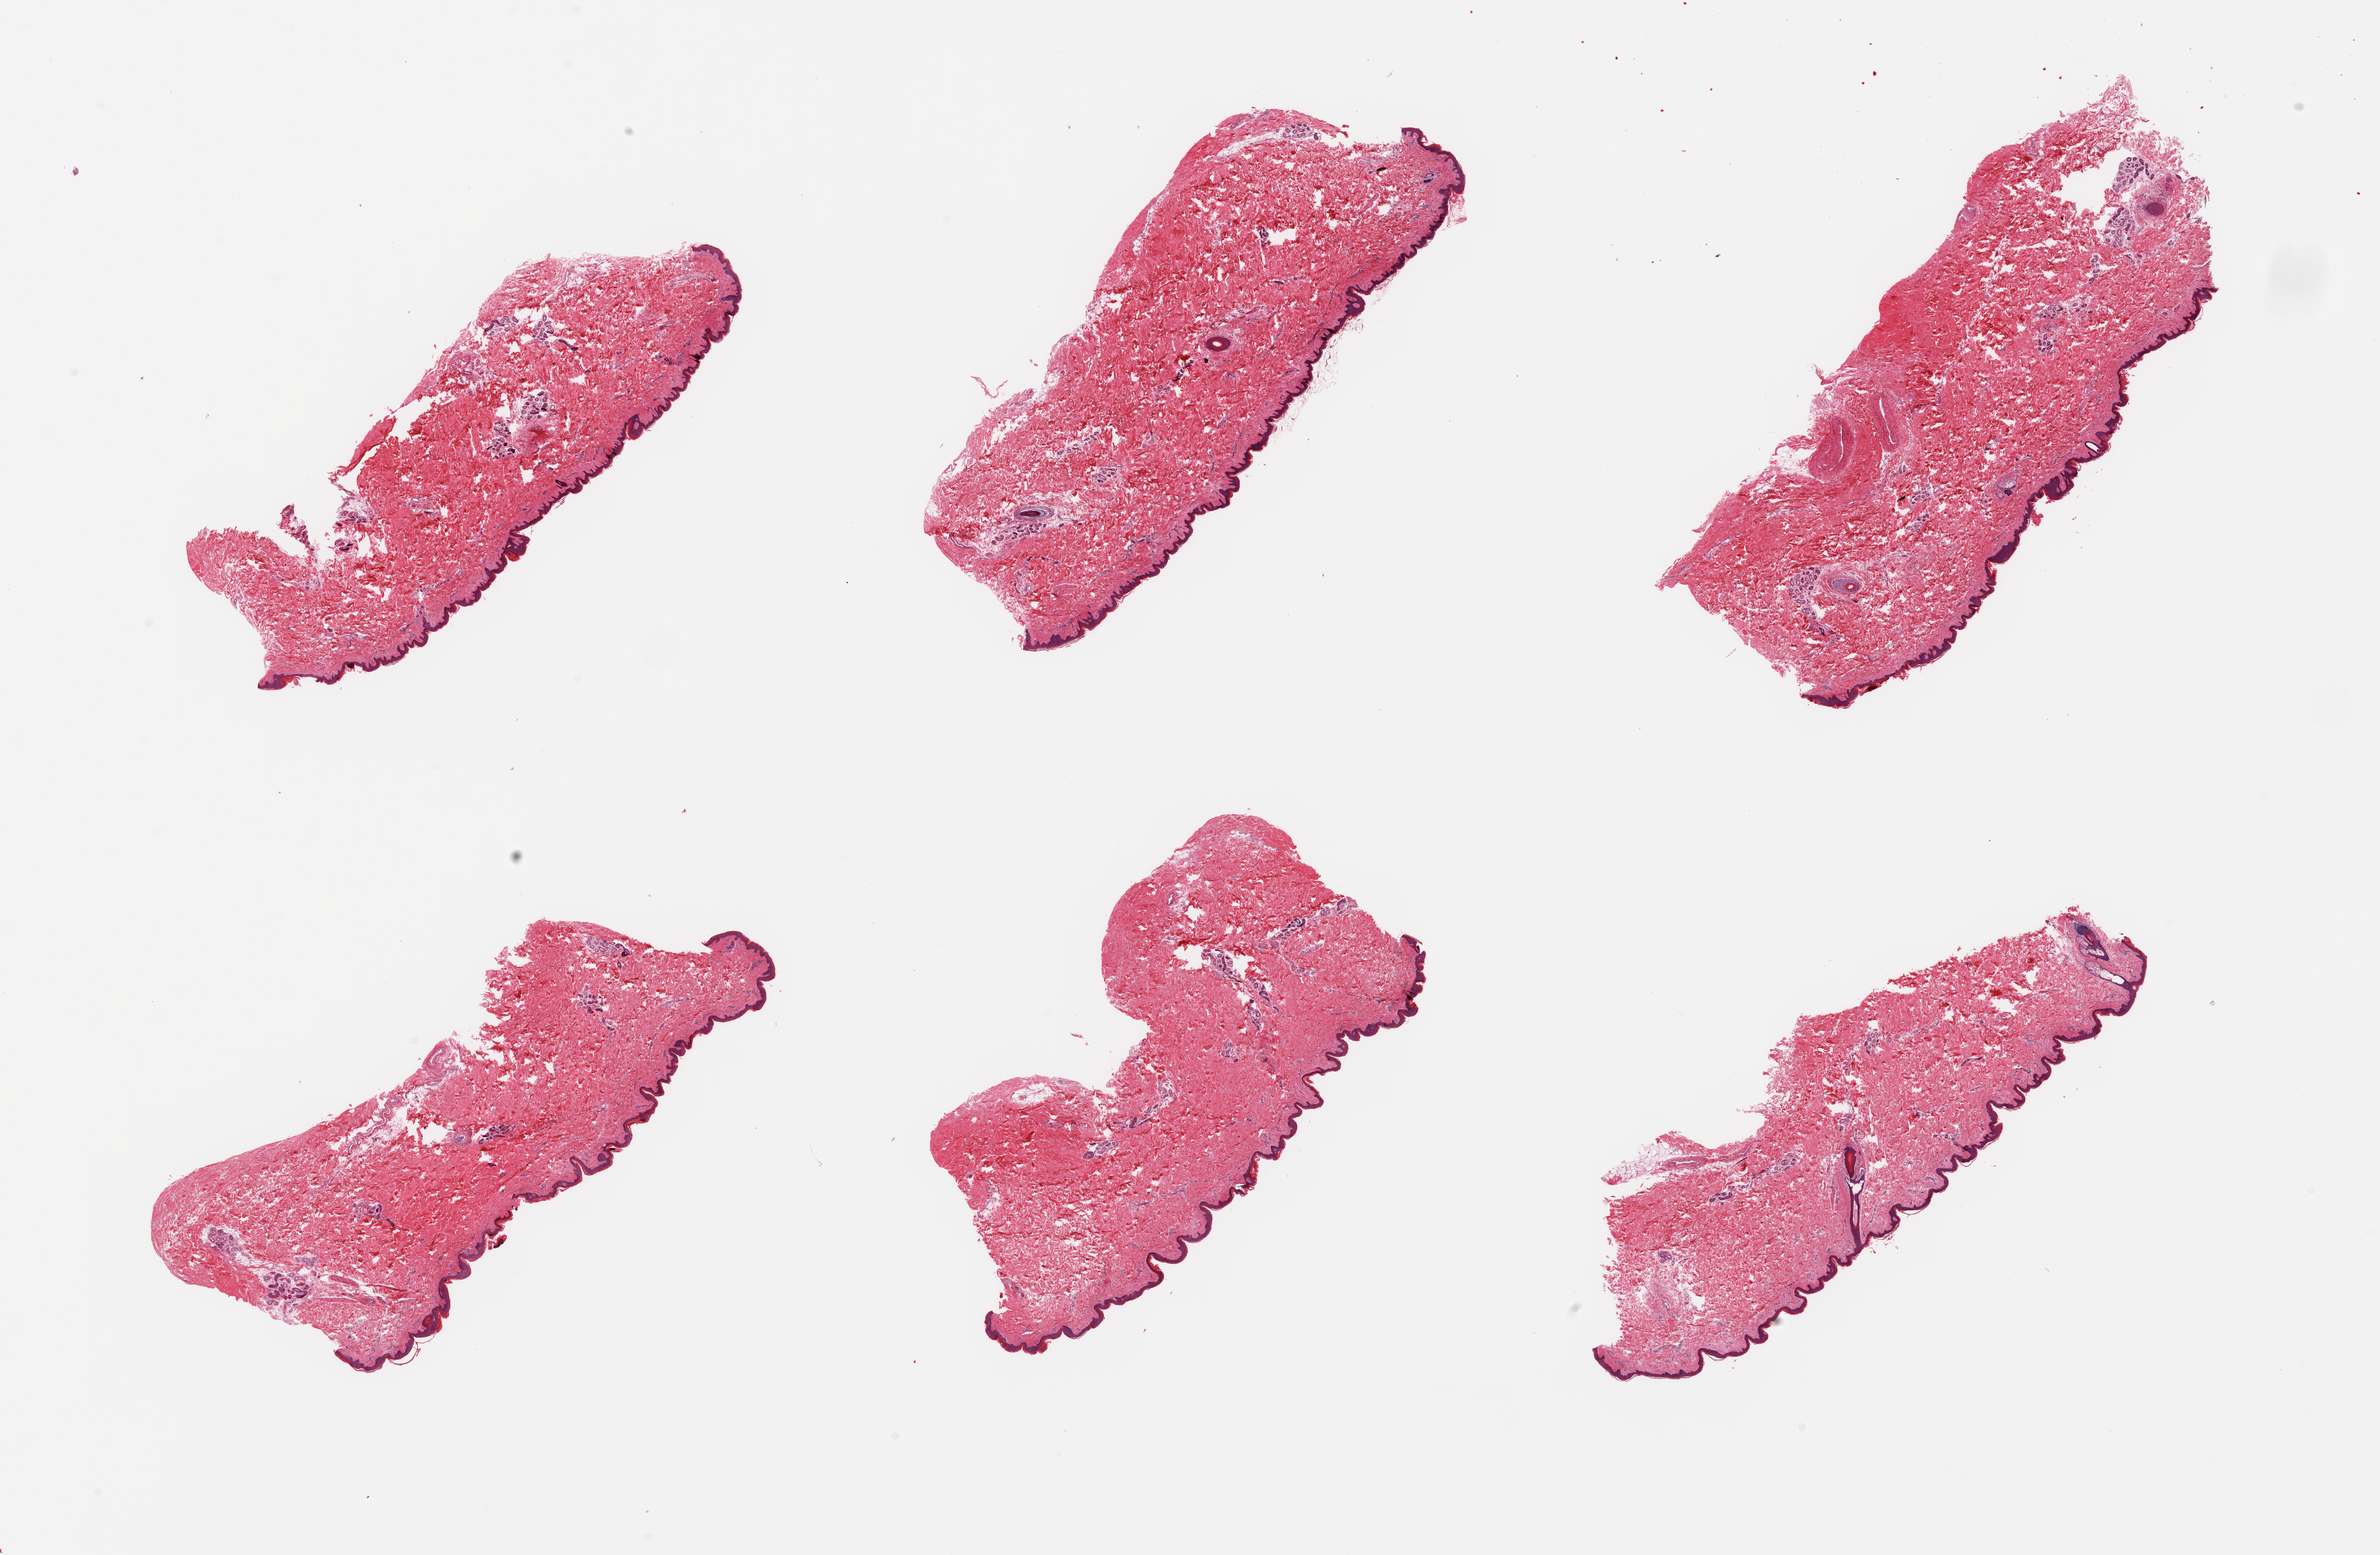
Digitized hematoxylin and eosin (H&E)-stained section, brightfield, shown as a low-resolution overview of the whole scanned area (about 26.6 x 17.4 mm, acquisition: 20x scan). PAXgene-fixed paraffin-embedded (PFPE) section. Sampled site (target tissue): skin of lower leg. Tissue donor sample. Male donor.
* review note (as recorded): 6 pieces; well trimmed, trivial fat only, epidermis measures 37 micorns